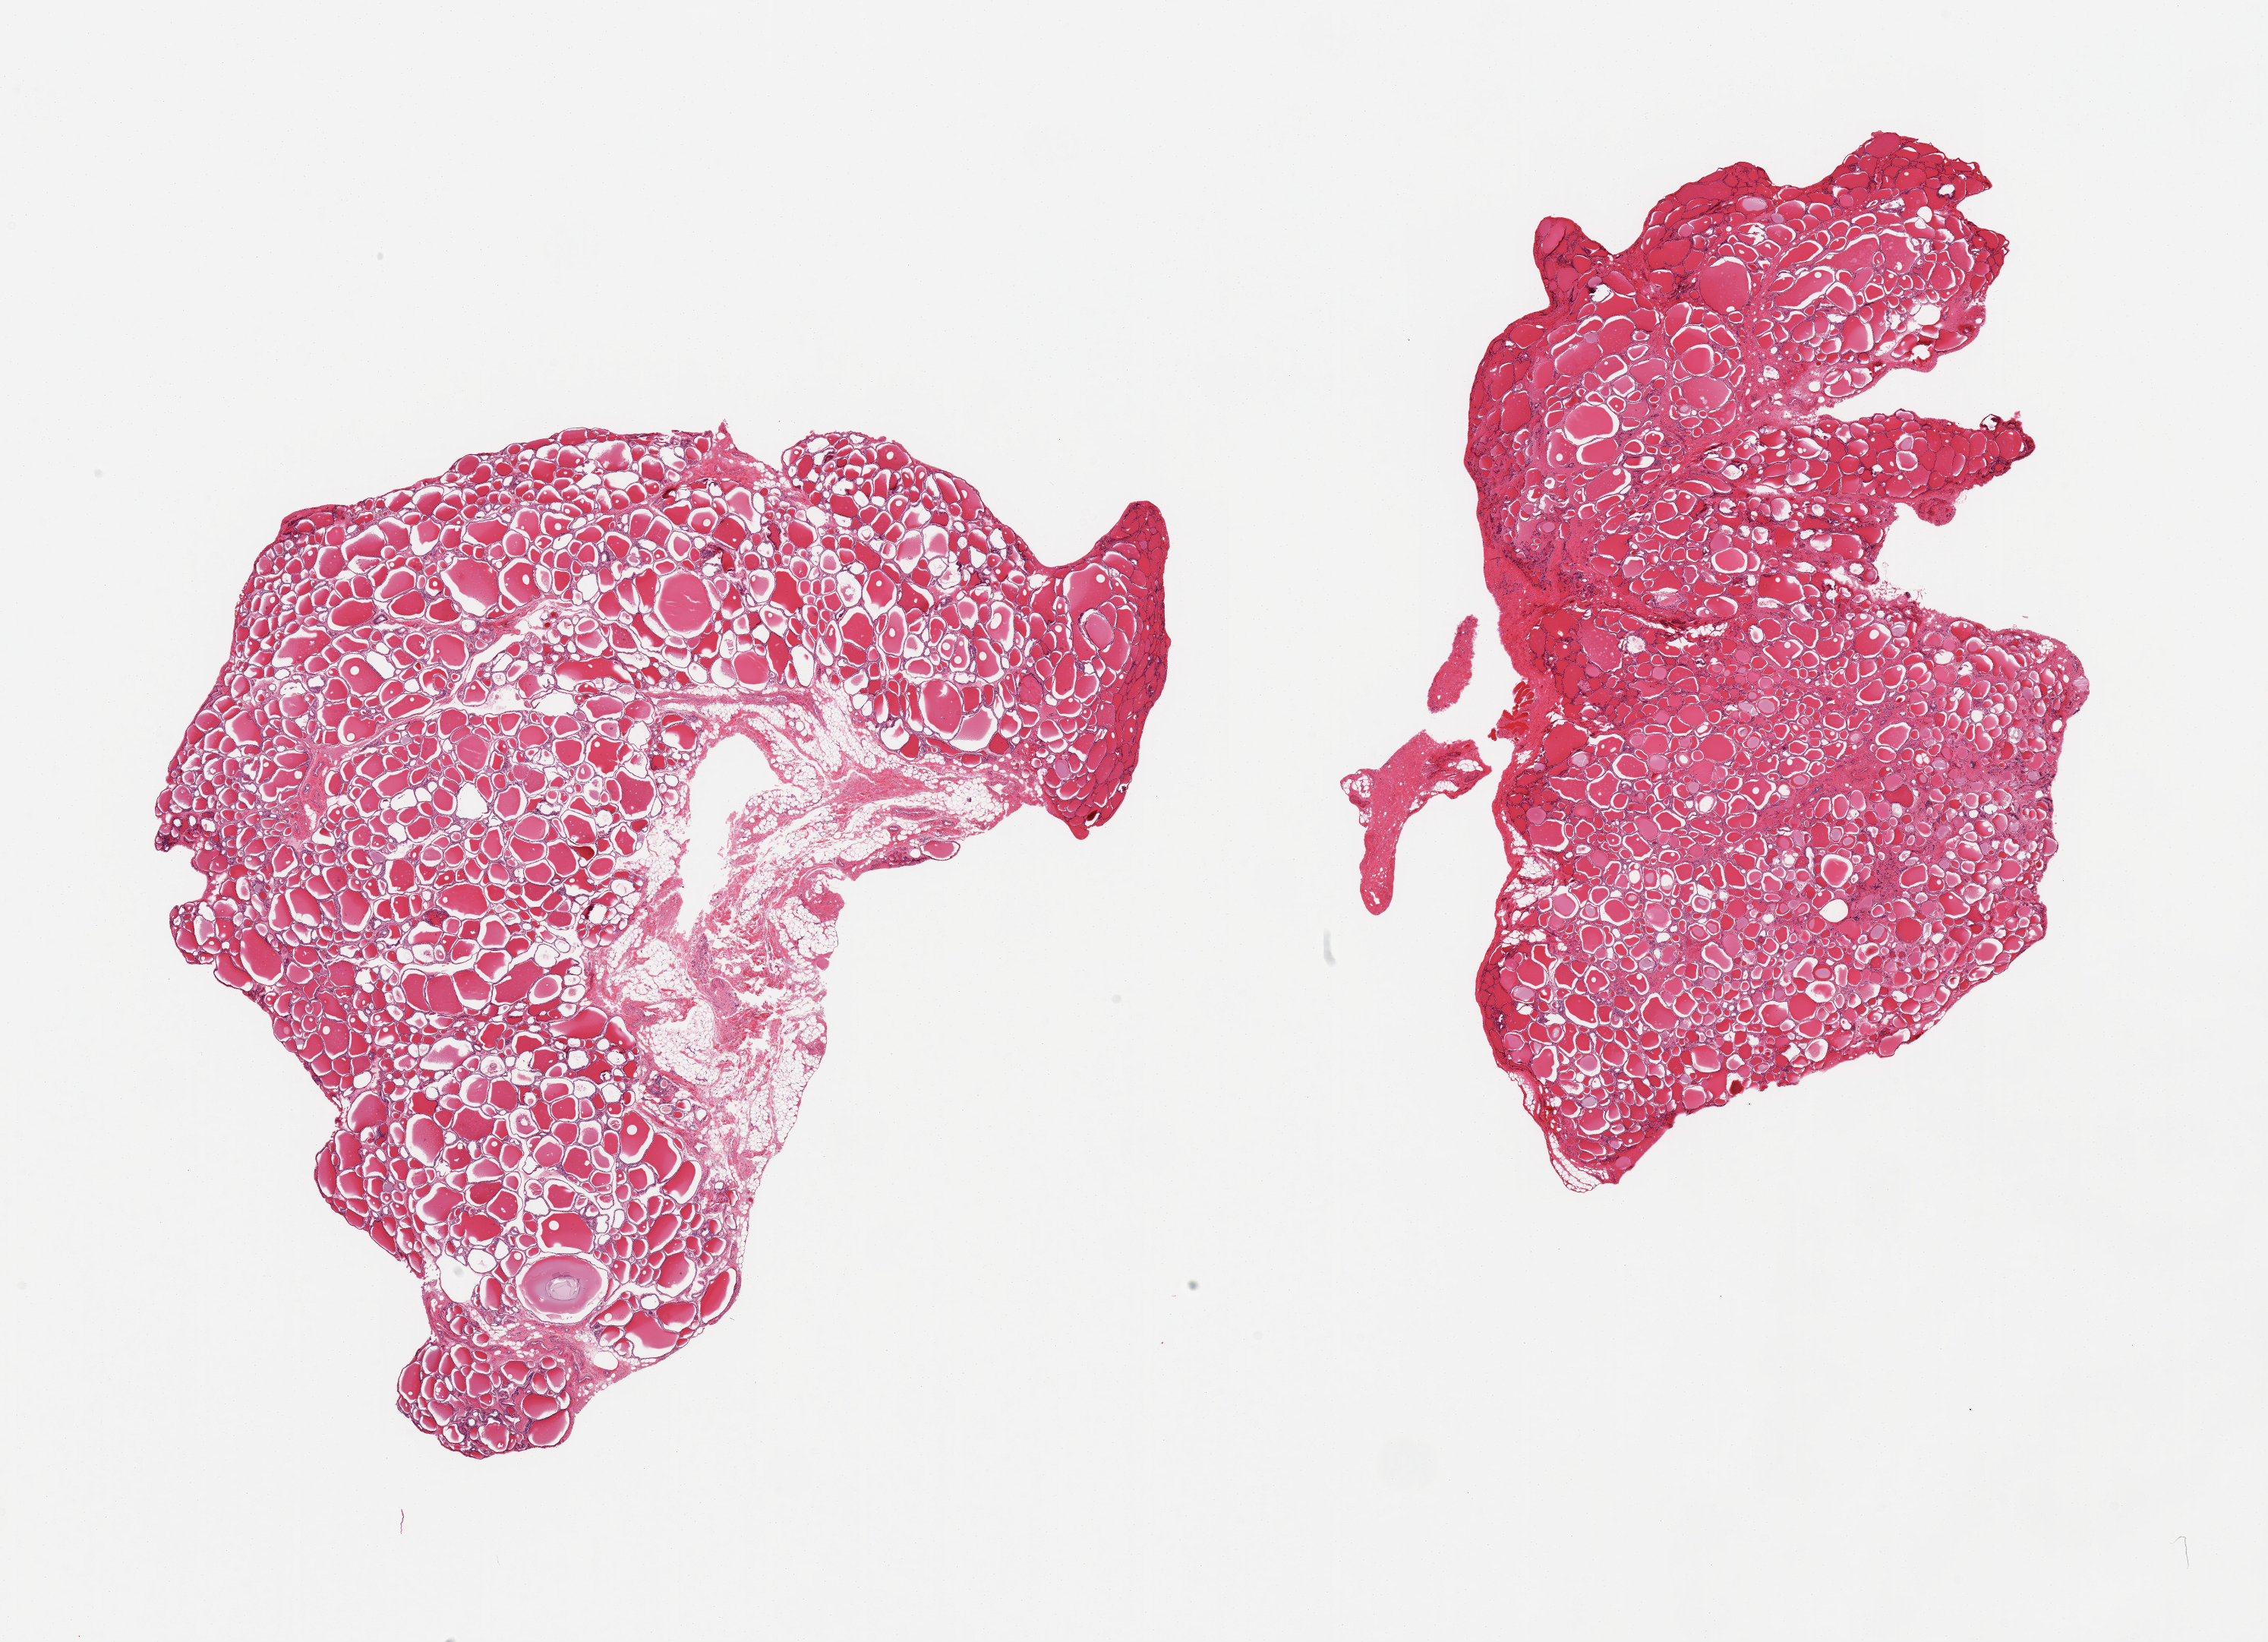
Hematoxylin and eosin (H&E) whole-slide image, a low-resolution overview of the entire scanned area, about 23.6 x 17.1 mm; PAXgene-fixed paraffin-embedded (PFPE) section; section of thyroid (target tissue); tissue donor sample. Male donor.
Pathologist's review note for this sample: 2 pieces; 0.6mm focus of skeletal muscle in fibrous capsule on edge of 1 piece.